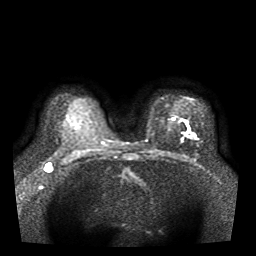
Breast MRI, one axial slice. Position 25 of 41 along the scan axis. Diffusion-weighted series; image 2 of 4 stored at this slice position (different b-values; order by instance number). 1.5 T. 5 mm slice thickness. 256 × 256 image matrix. Female patient.
Outlined on this slice (expert manual segmentation):
- tumour on diffusion-weighted imaging: bounding box [x1, y1, x2, y2] px = [193, 135, 197, 138]